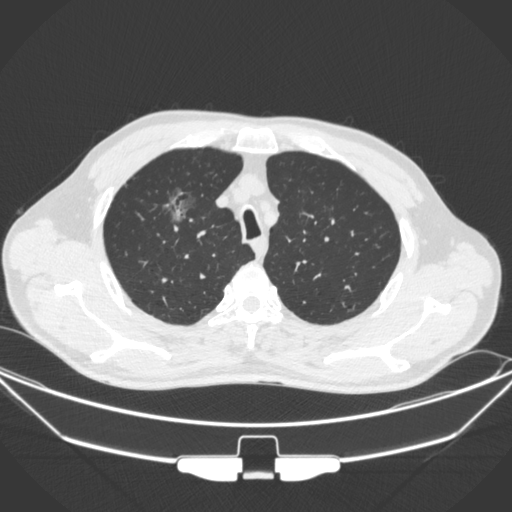
Chest CT, one axial slice; position 277 of 355 along the scan axis; lung window (W 1500 / L -600 HU); 1 mm slice thickness; 512 × 512 image matrix. Male patient, age 67 years. Case-level facts recorded for this patient, not image findings: clinical TNM (as recorded): T1c N0 M0; histopathological grade: G2.
Annotated regions visible in this slice (rectangle marked by the reading radiologist):
- lung tumour (recorded histology: adenocarcinoma): bounding box (x1, y1, x2, y2) in pixels: (159, 182, 194, 226)